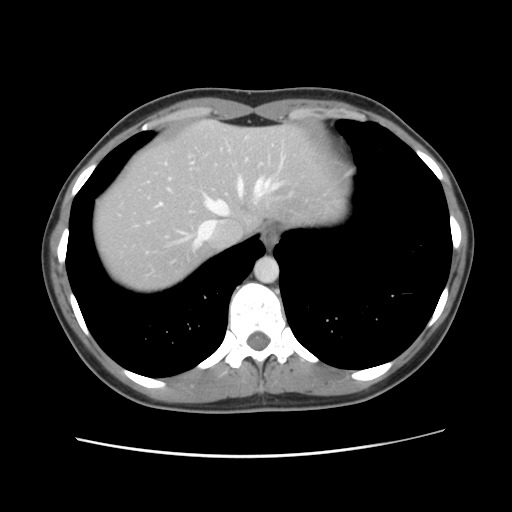
Contrast-enhanced abdominal CT, one axial slice. Slice 104 of 134 in the series (ordered by position). 120 kVp. Intravenous contrast given. Soft-tissue window (W 400 / L 40 HU). 2.5 mm slice thickness. 512 × 512 image matrix. Female patient, age 33 years. Case-level facts recorded for this patient, not image findings: diagnosis: colorectal cancer liver metastases, imaged before liver resection; multiple liver metastases: yes; largest metastasis: 4.5 cm; chemotherapy before resection: no.
Outlined on this slice (manually delineated by an expert):
- hepatic veins: bounding box <160,179,281,247> (left, top, right, bottom; pixels)
- liver: <92,121,334,293>
- planned liver remnant (the part of the liver to remain after resection): <93,121,334,294>